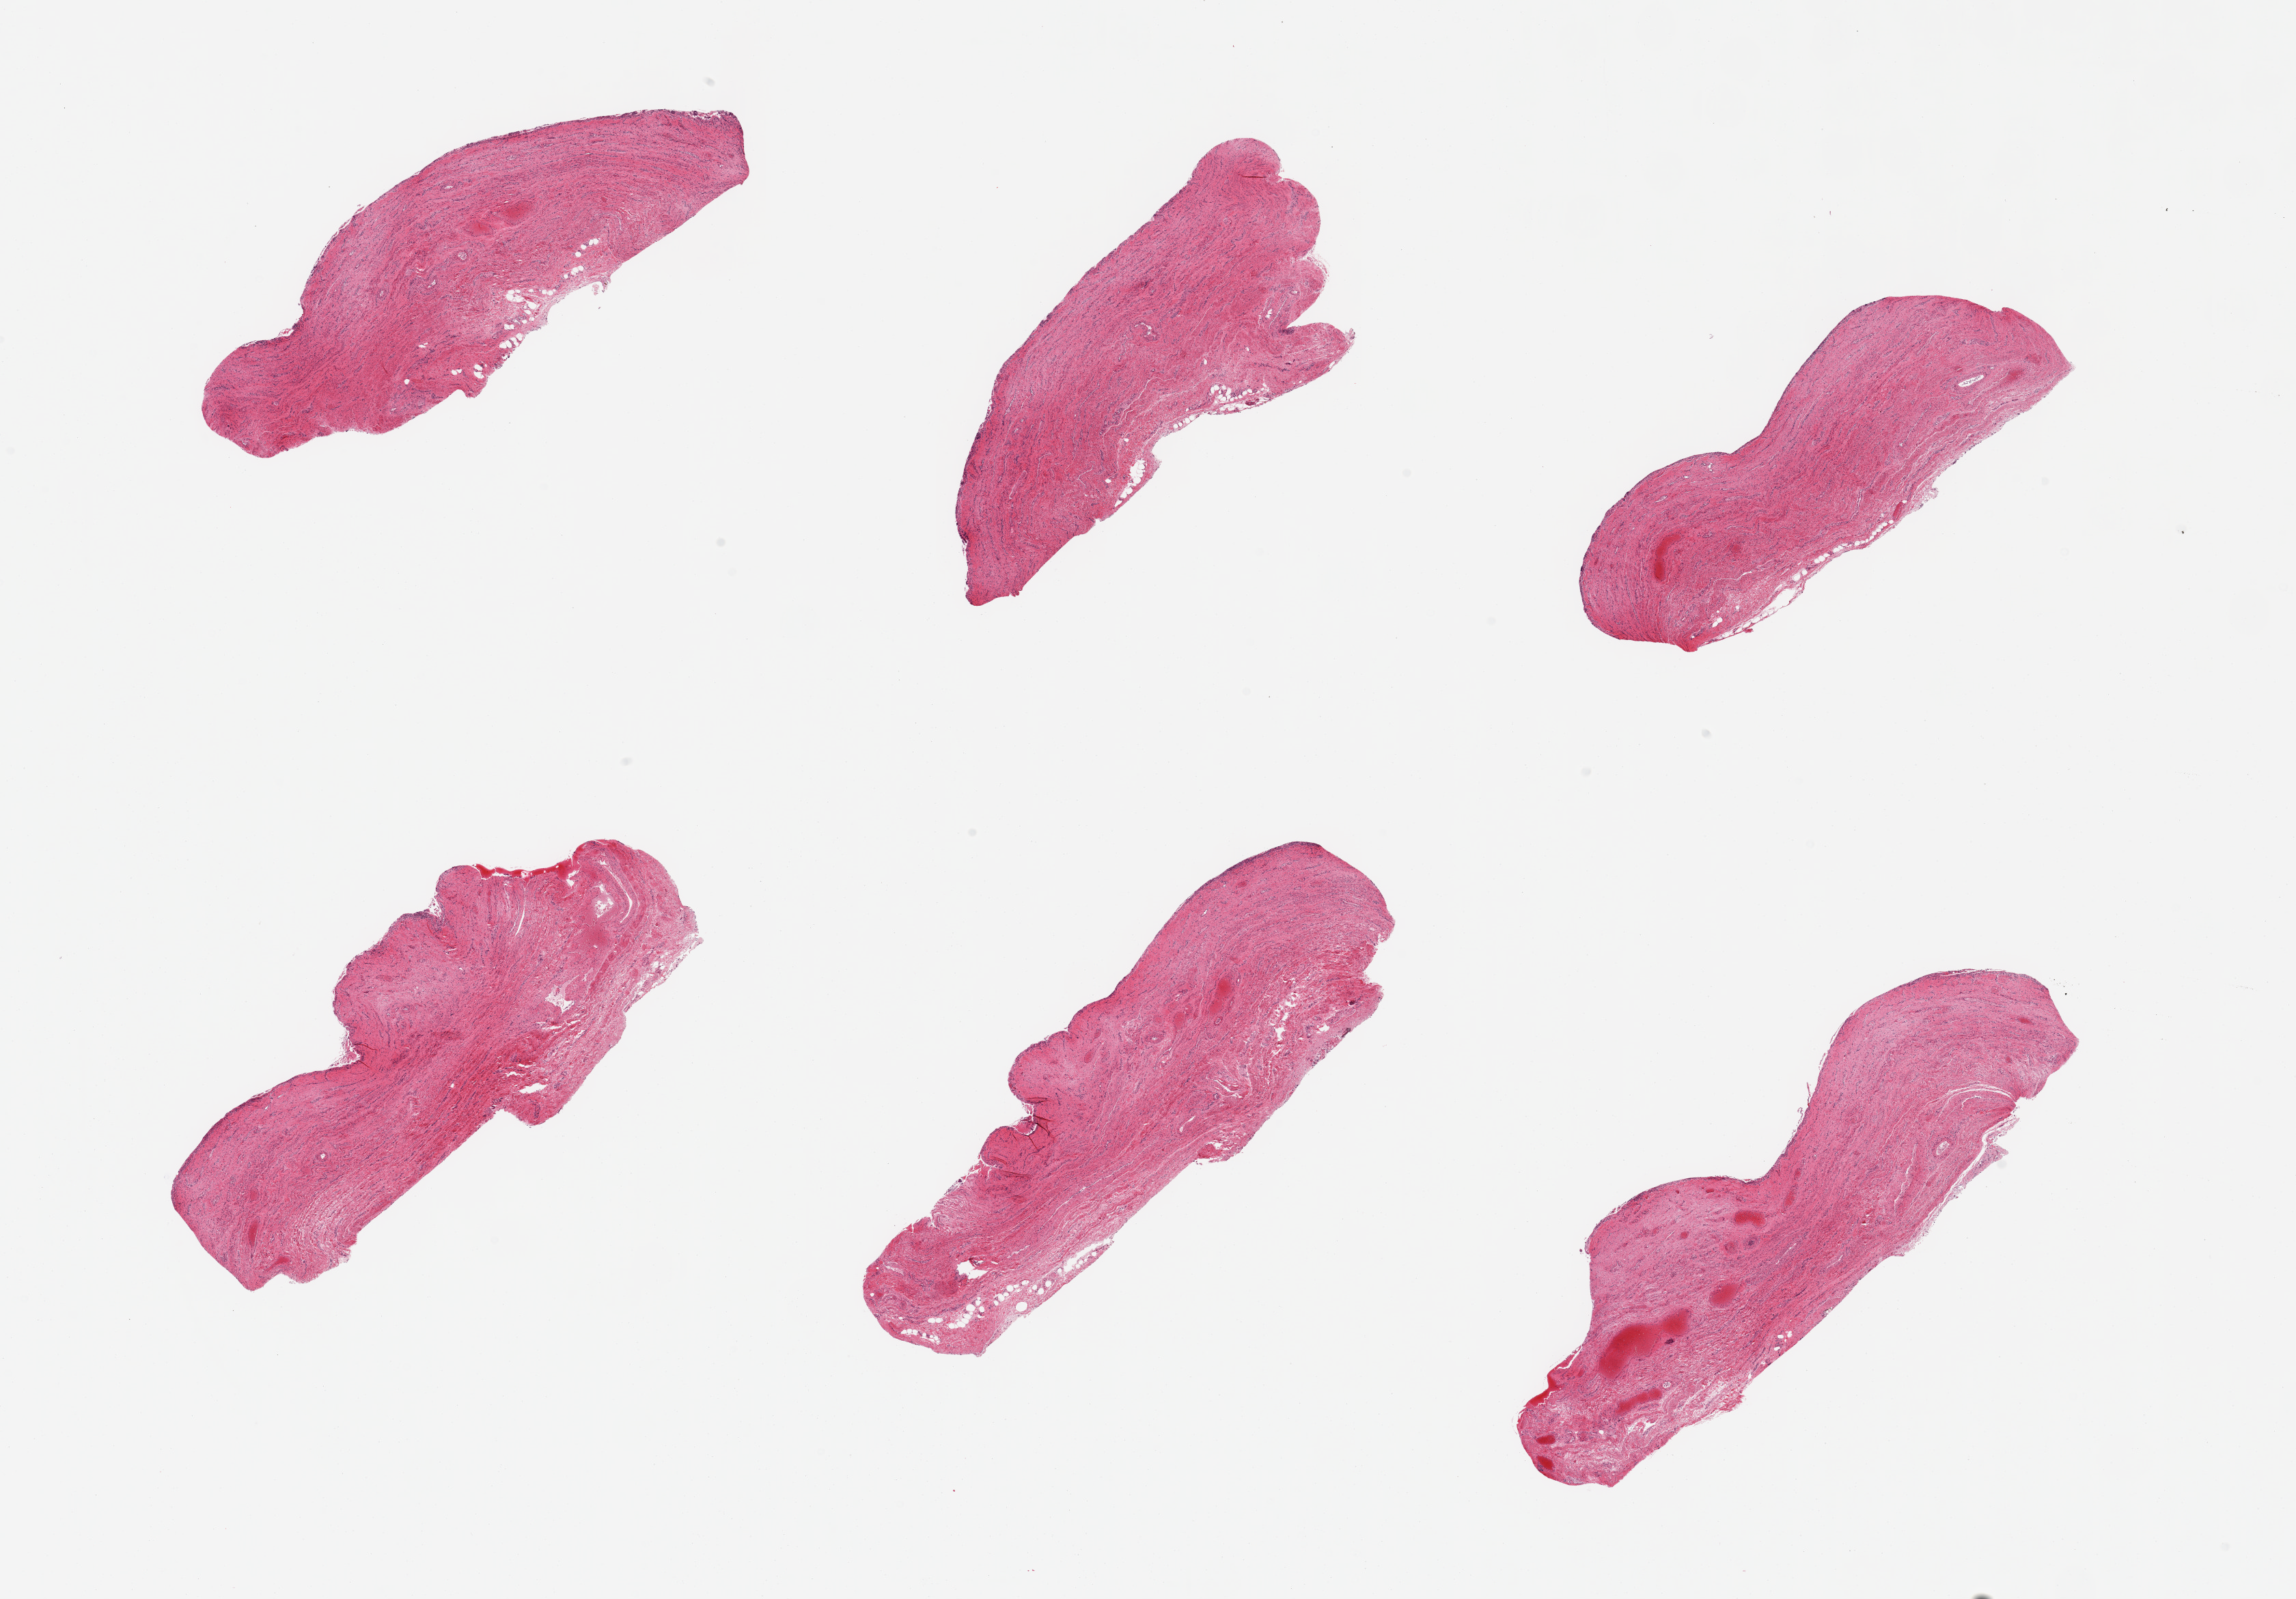
Haematoxylin and eosin whole-slide image — shown as a low-resolution overview of the whole scanned area (about 26.6 x 18.5 mm, from a 20x scan), PAXgene-fixed, paraffin-embedded tissue, sampled site (target tissue): vagina, tissue donor sample. Female donor.
Review note (as recorded): 6 pieces; epithelium is denuded/autolyzed.